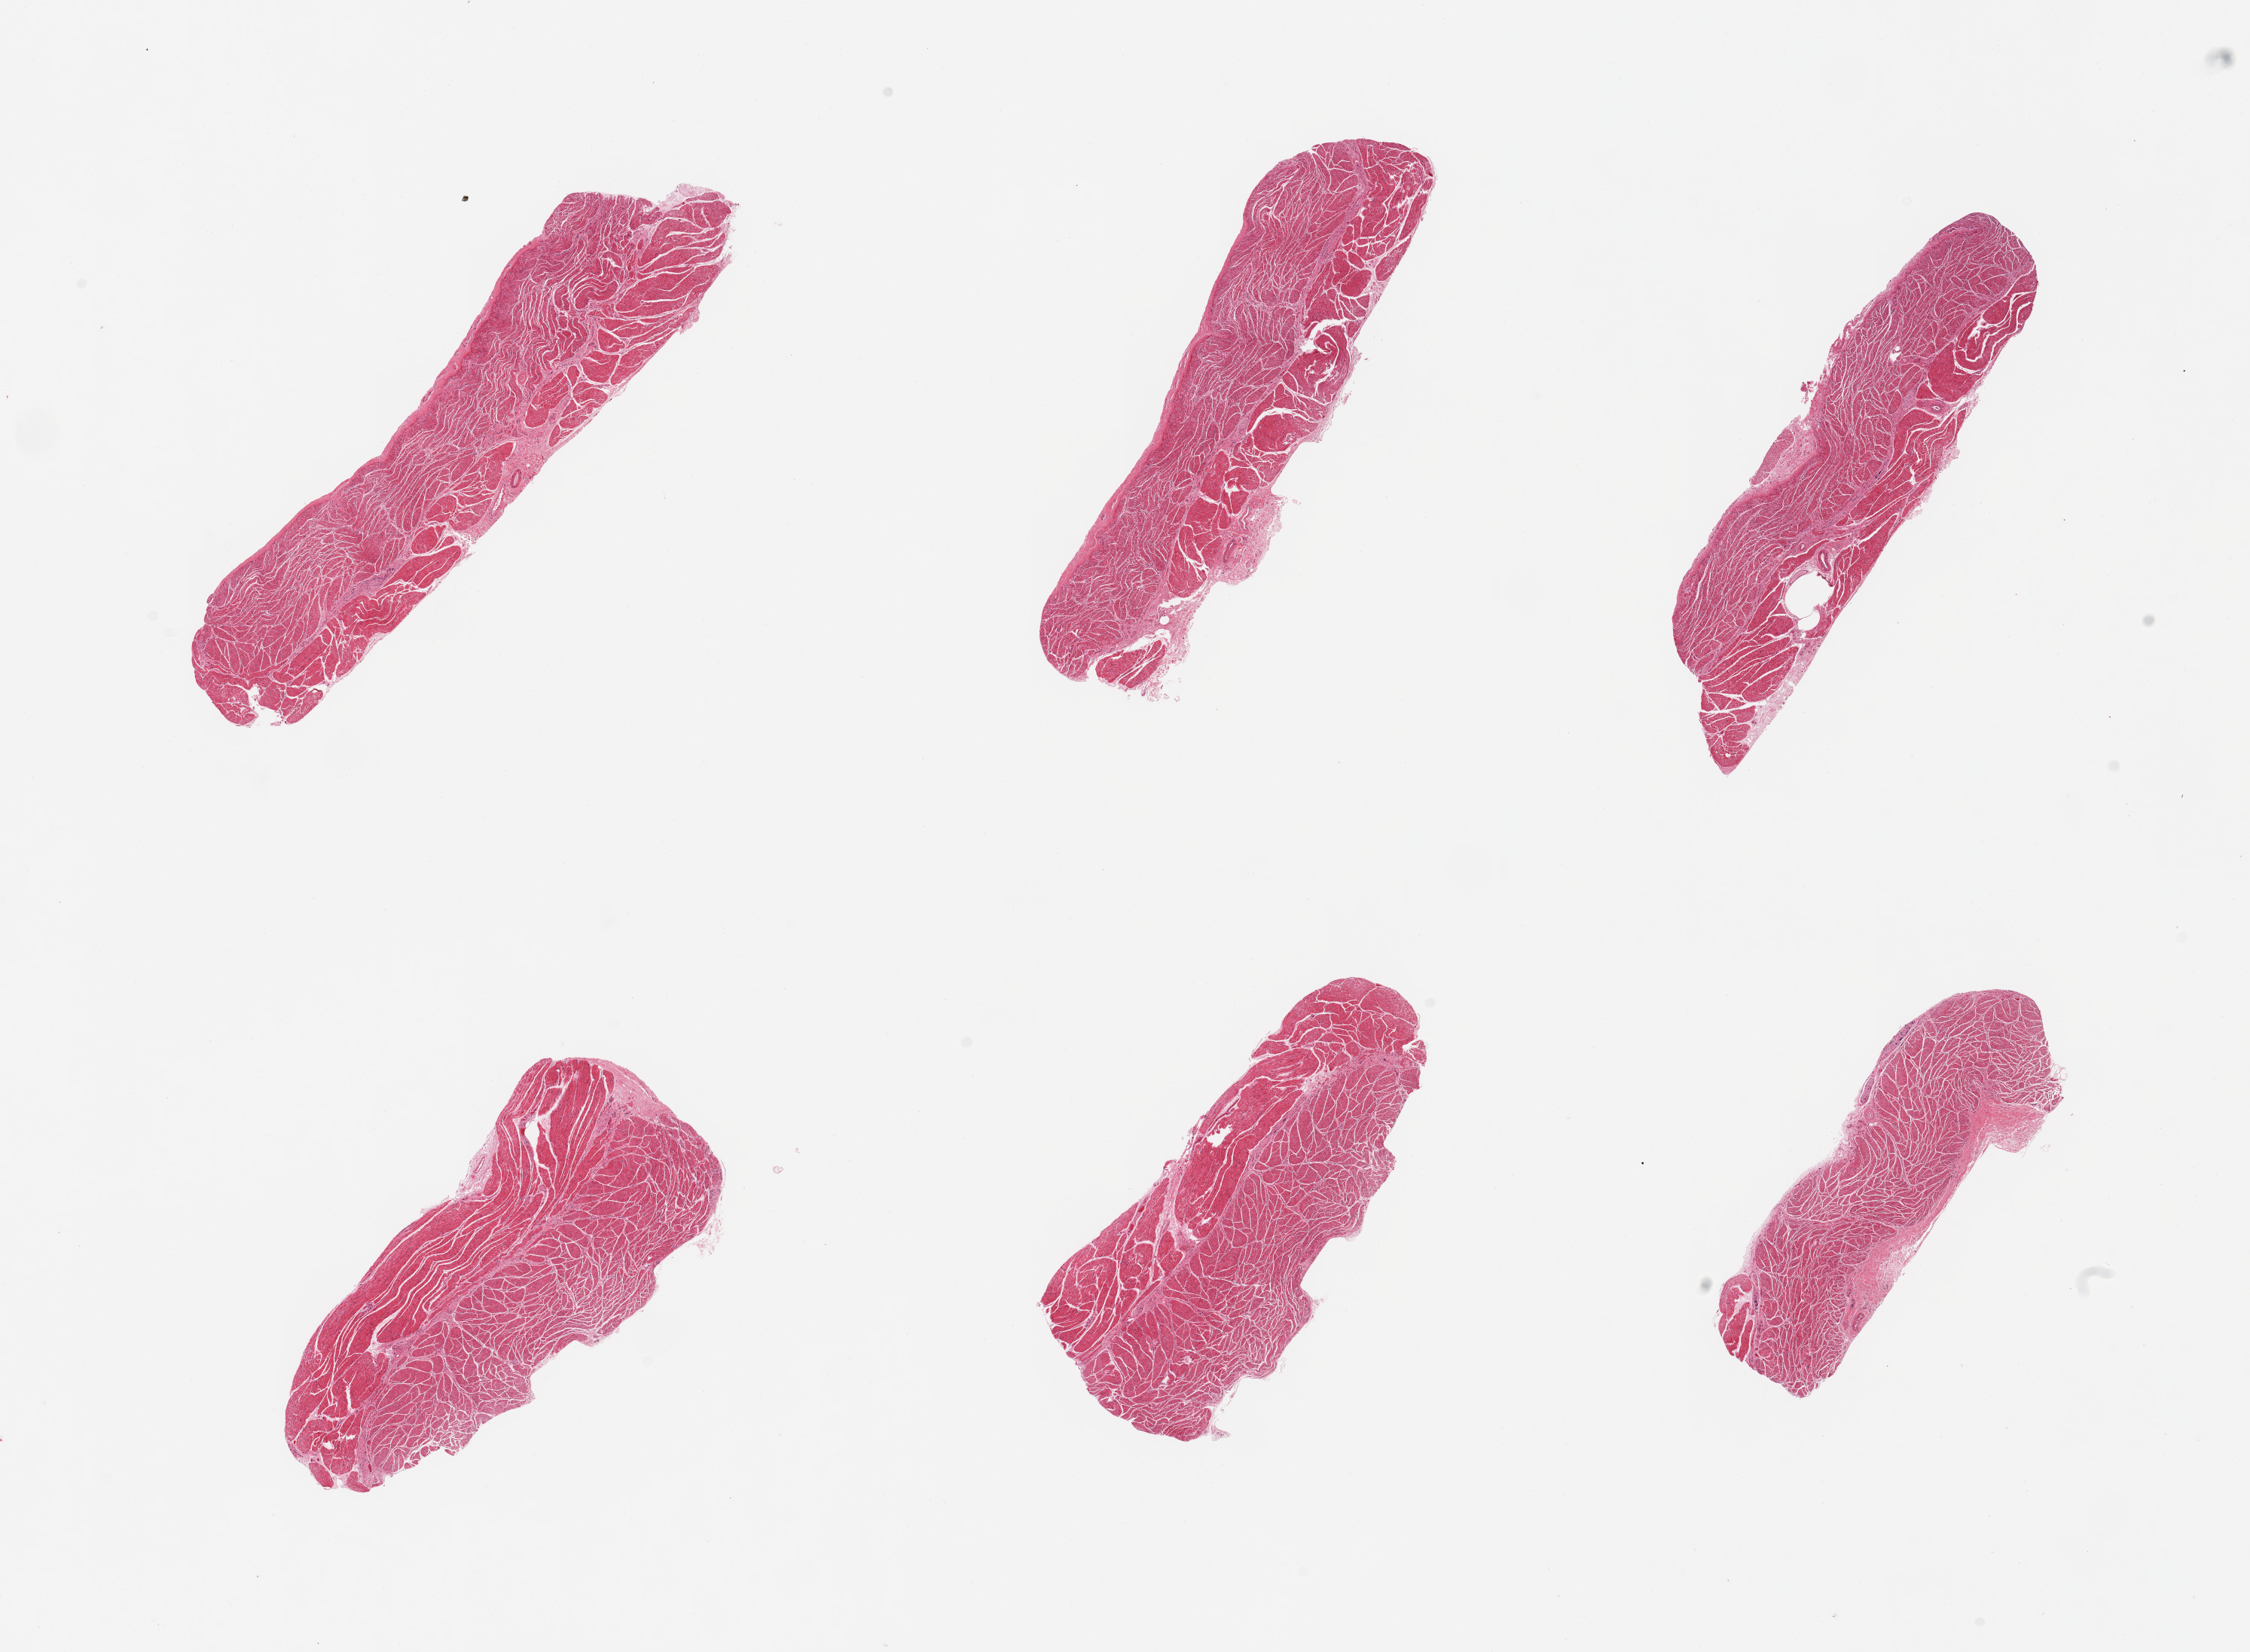
Digitized H&E-stained section, brightfield — a low-resolution overview of the entire scanned area, about 23.6 x 17.3 mm; PAXgene-fixed paraffin-embedded (PFPE) section; sampled site (target tissue): esophageal muscle; donor tissue sample. Donor: male.
Pathologist's review note for this sample: 6 pieces; well trimmed.